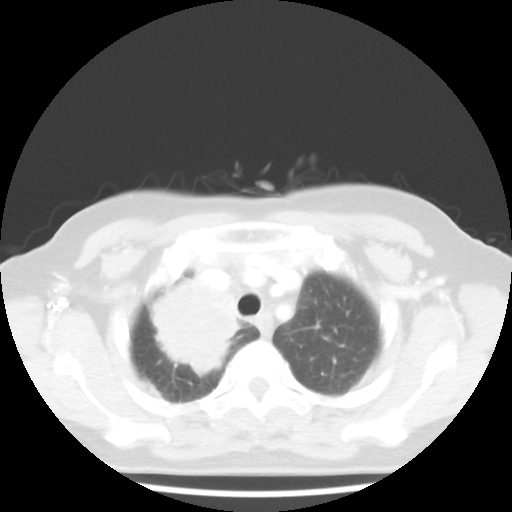
Chest CT, one axial slice; slice 37 of 44 in the series (ordered by position); reconstruction kernel STANDARD; 100 kVp; lung window (W 1500 / L -600 HU); 512 × 512 image matrix, field of view 316 × 316 mm. Female patient, age 62 years. Case-level facts recorded for this patient, not image findings: clinical TNM (as recorded): T3 N0 M0; histopathological grade: G3.
Structures marked on this image (bounding box drawn by a radiologist):
- lung tumour (recorded histology: small cell carcinoma): bounding box (x1, y1, x2, y2) in pixels: (138, 263, 258, 383)